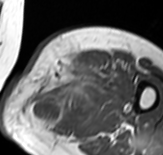
MRI of an extremity soft-tissue mass, one axial slice. Position 44 of 65 along the scan axis. MR volume resampled by the dataset authors to the PET/CT grid (not the native acquisition matrix). 3.27 mm slice thickness. 163 × 155 image matrix. Female patient. From the clinical record (not read from this slice): histological type: pleomorphic leiomyosarcoma; grade: high; site of the primary tumour: left thigh.
Outlined on this slice (expert contour drawn on MRI and transferred to this co-registered scan by the dataset authors):
- gross tumour volume including surrounding oedema: box from (x=26, y=58) to (x=104, y=134) px
- gross tumour volume (mass): (x=53, y=58)–(x=93, y=102)